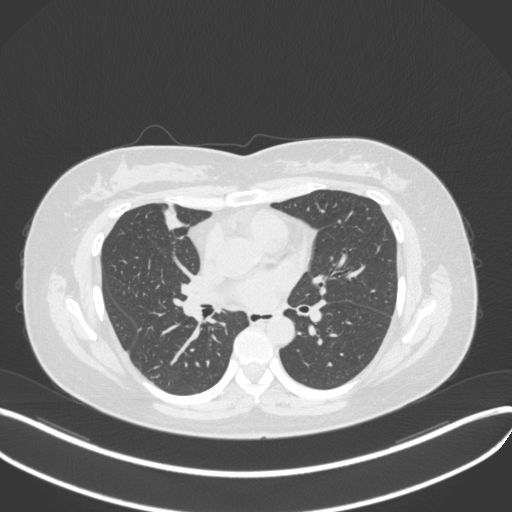
Chest CT, one axial slice. Position 164 of 272 along the scan axis. Reconstruction kernel B31f. Lung window (W 1500 / L -600 HU). 1 mm slice thickness. 512 × 512 image matrix, field of view 400 × 400 mm. Female patient, age 42 years. From the clinical record (not read from this slice): clinical TNM (as recorded): T1b N0 M0.
Outlined on this slice (rectangle marked by the reading radiologist):
- lung tumour (recorded histology: adenocarcinoma): box from (x=158, y=208) to (x=188, y=237) px